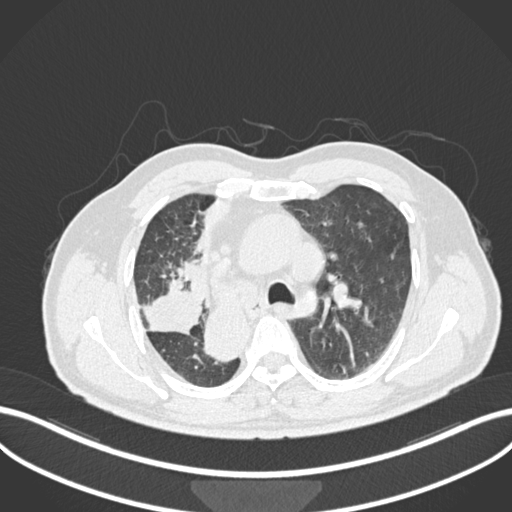
Chest CT, one axial slice. Slice 161 of 206 in the series (ordered by position). Reconstruction kernel B30f. Lung window (W 1500 / L -600 HU). 512 × 512 image matrix. Male patient, age 67 years. From the clinical record (not read from this slice): clinical TNM (as recorded): T2a N0 M0.
Structures marked on this image (bounding box drawn by a radiologist):
- lung tumour (recorded histology: squamous cell carcinoma): box from (x=134, y=270) to (x=203, y=339) px